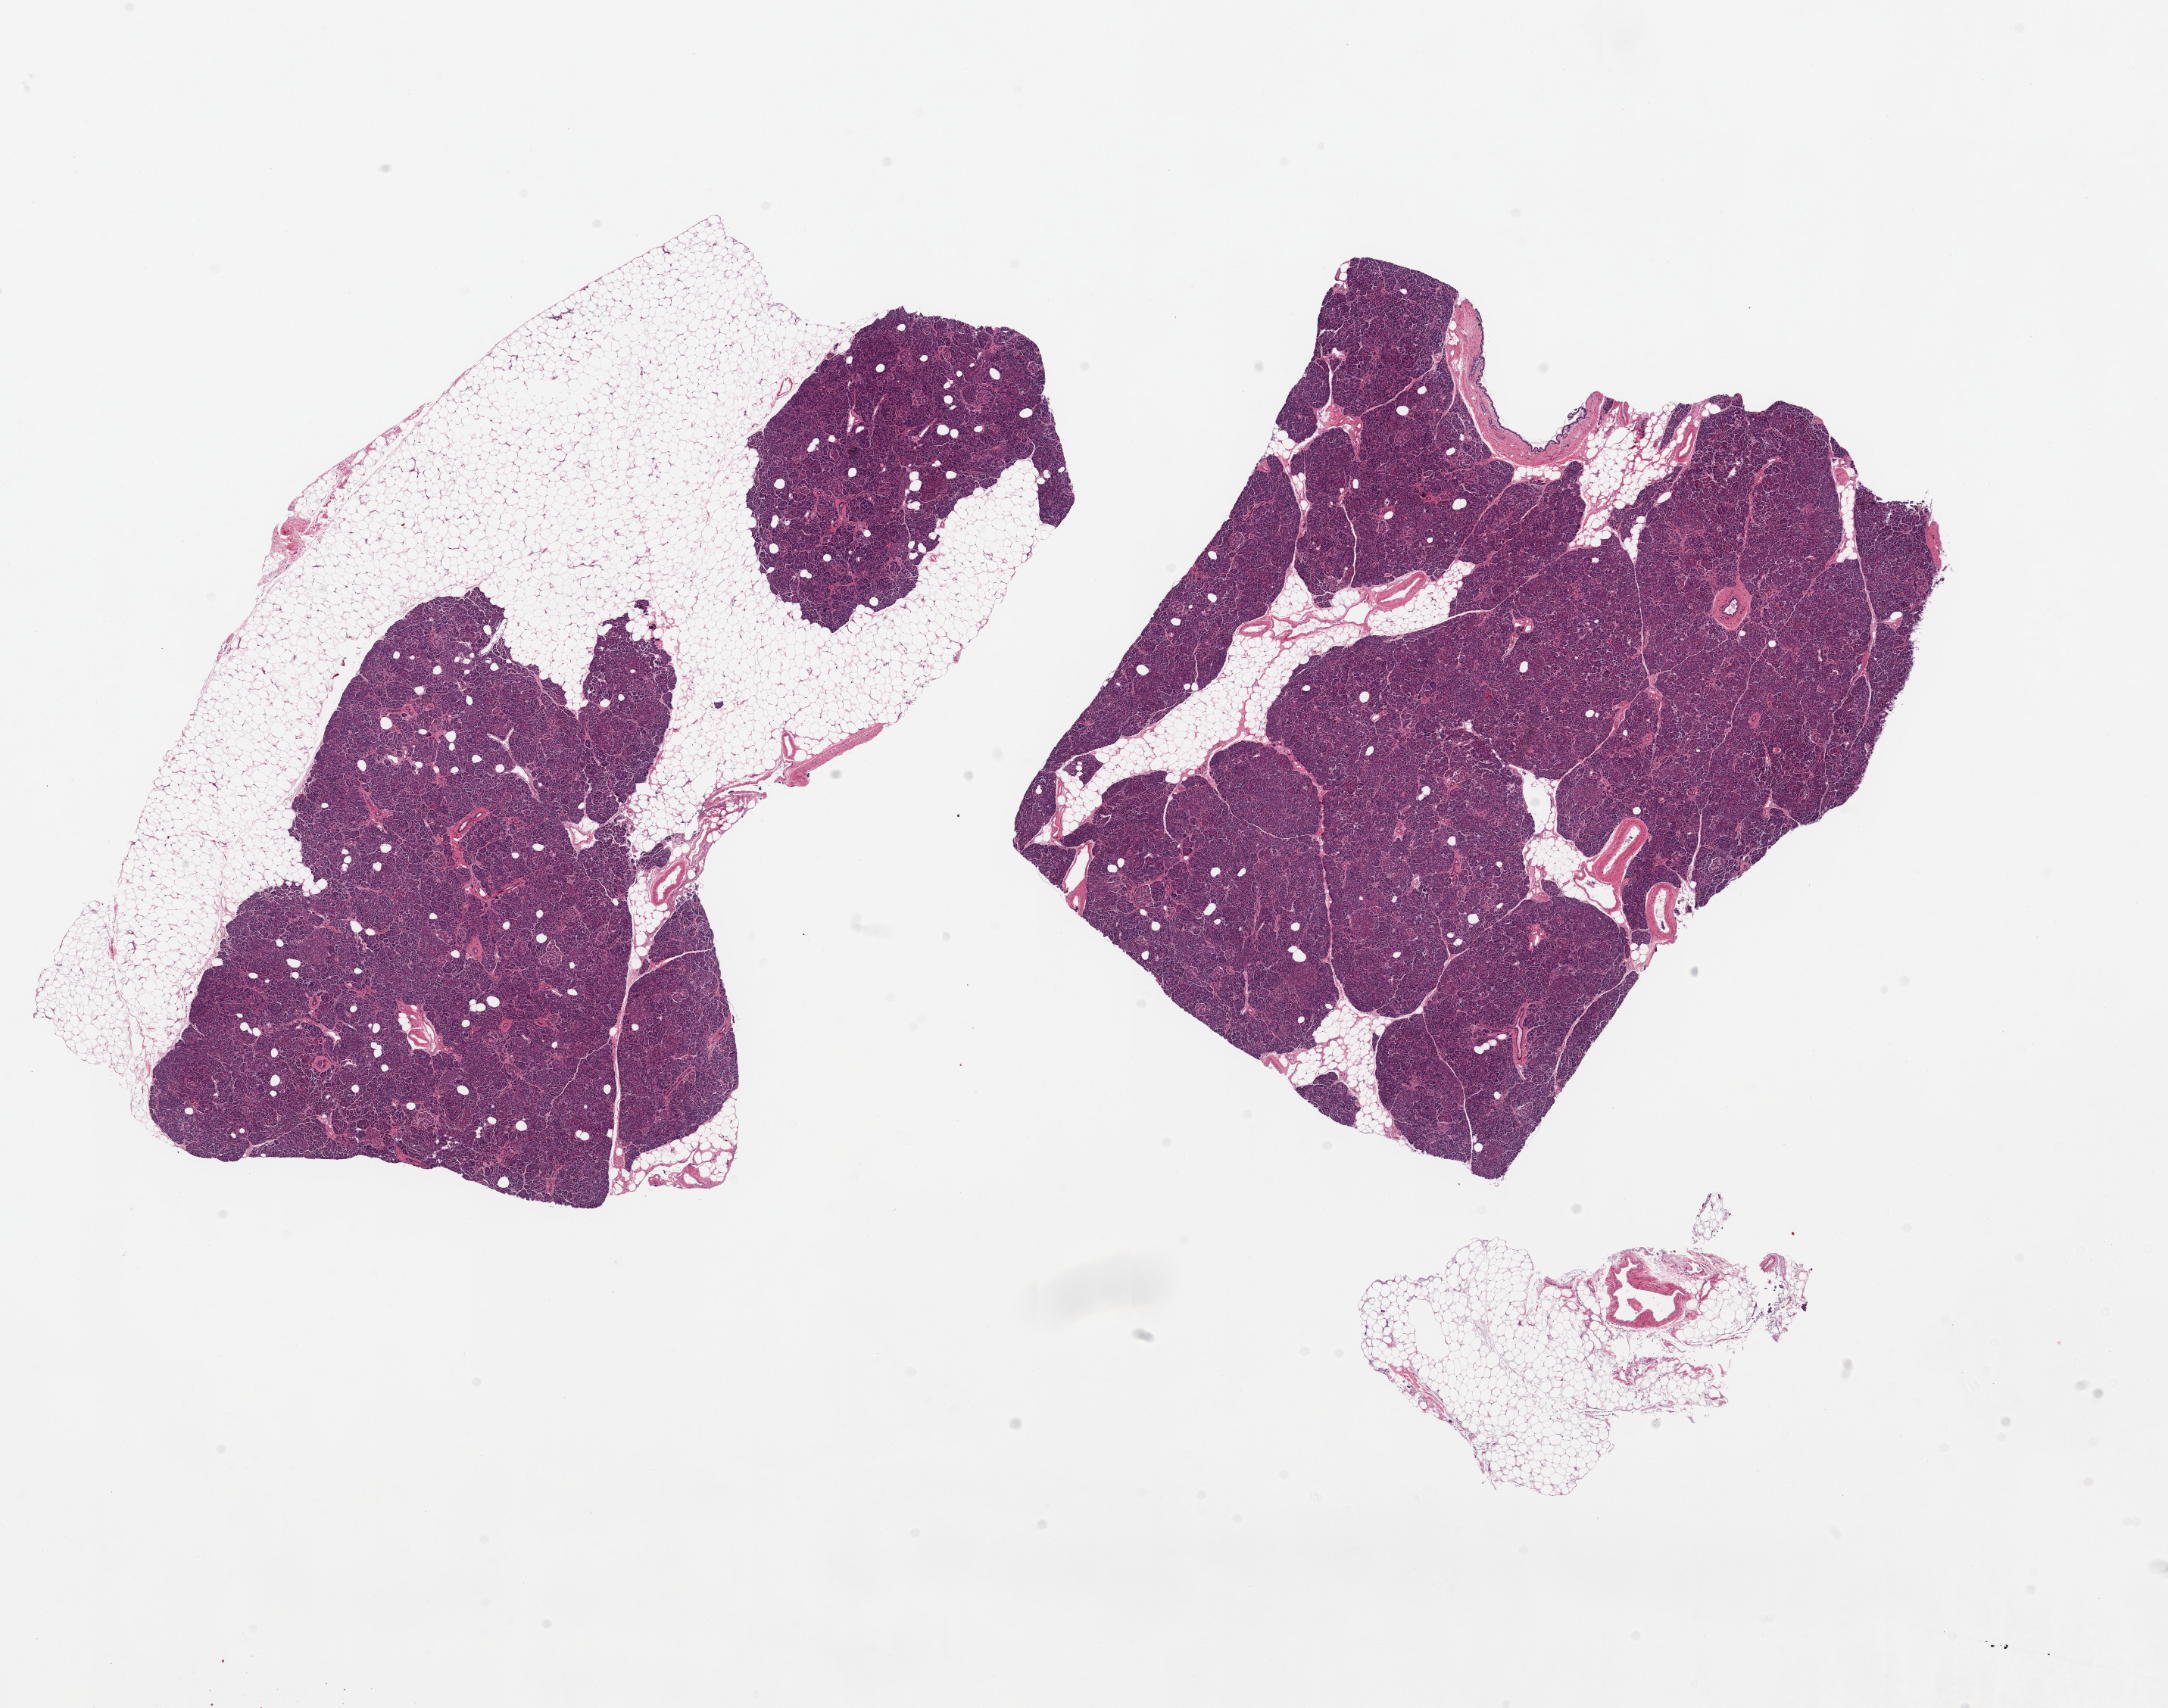
Hematoxylin and eosin (H&E) whole-slide image, a low-resolution overview of the entire scanned area, about 22.6 x 17.8 mm (slide scanned at 20x), PAXgene-fixed paraffin-embedded (PFPE) section, section of pancreas (target tissue), tissue donor sample.
Review note (as recorded): 2 pieces, adherent/interstitial fat is ~35-40%; Islets well visualized.